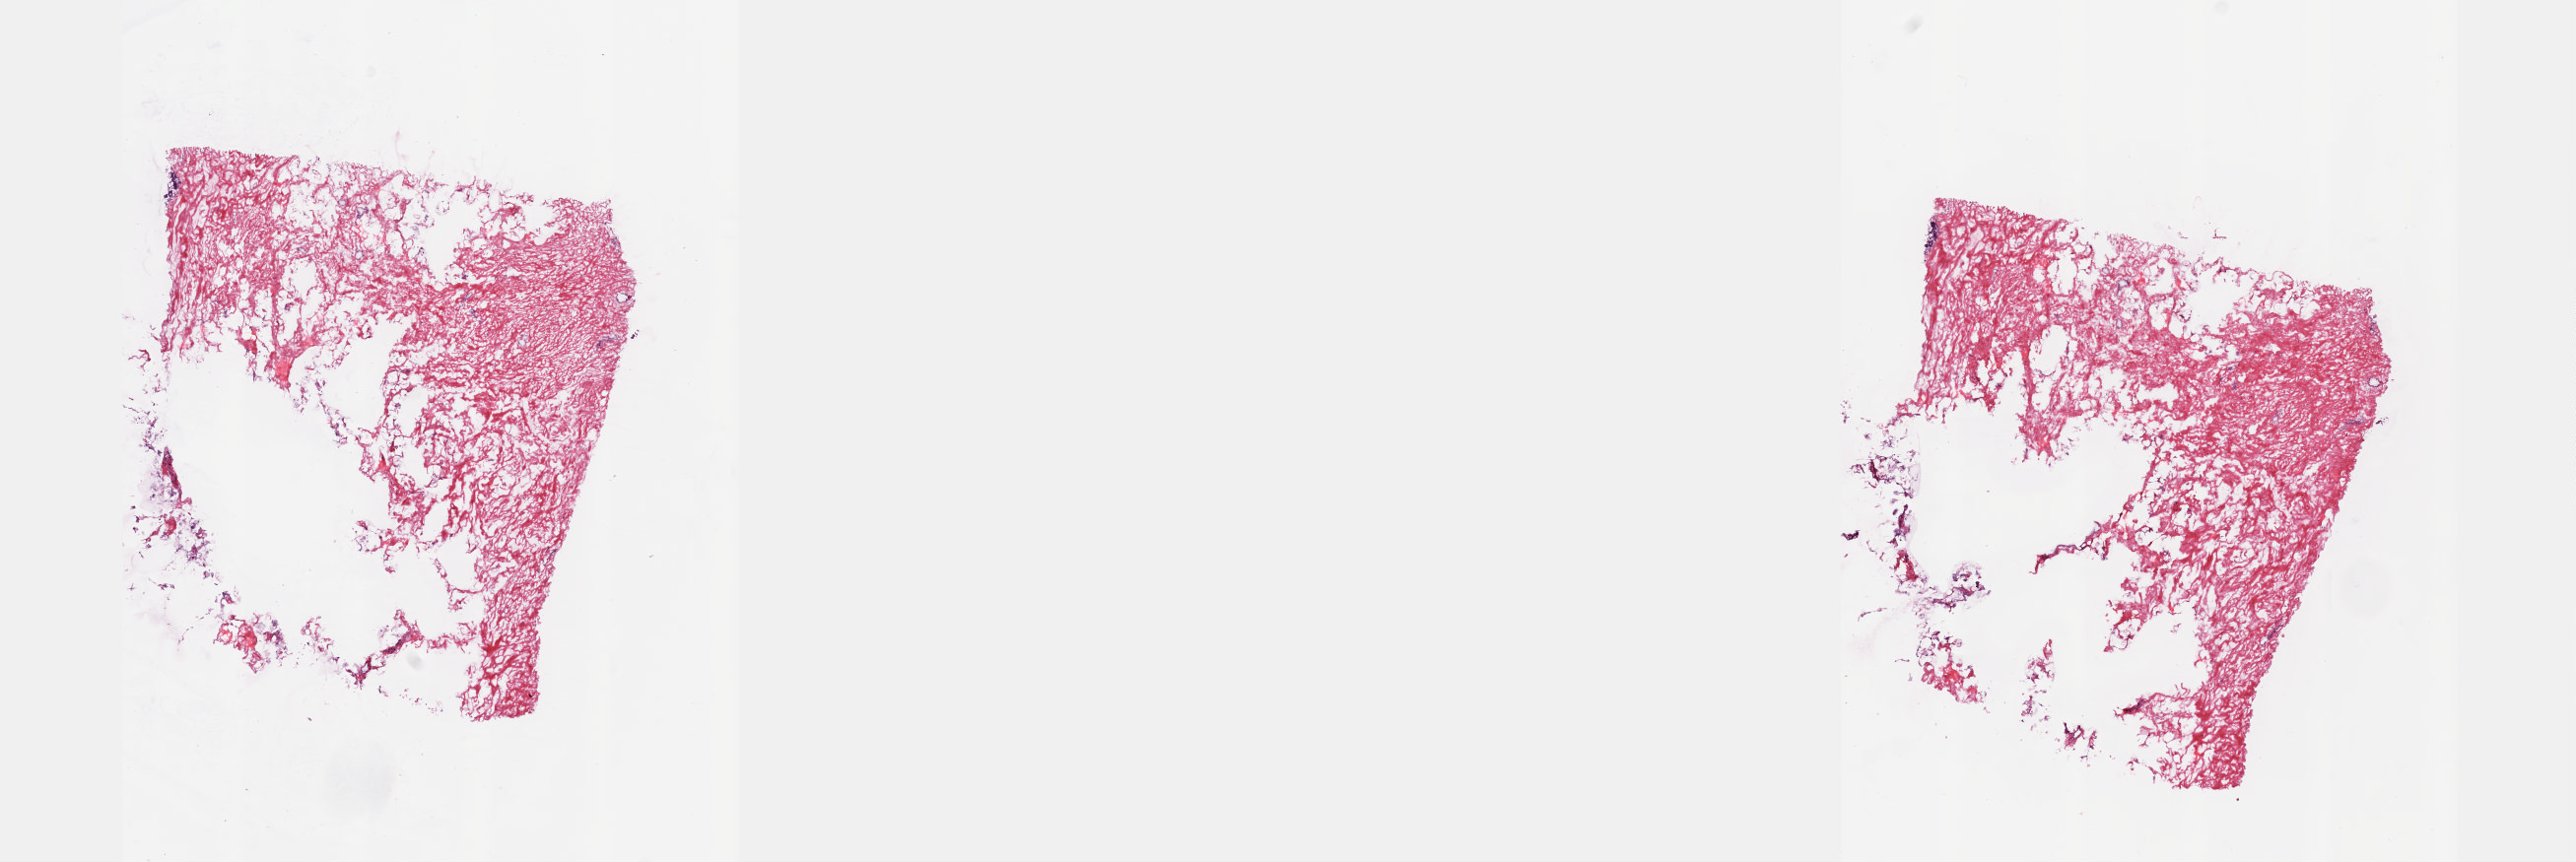
Whole-slide histology image, H&E, low-resolution overview of the scanned area, about 21.1 x 7.1 mm (from a 20x scan); frozen section; solid tissue normal (non-tumour tissue) sample from the breast. Patient: female, age at initial diagnosis 46 years. Pathologist review of this section (percent, as recorded): tumour cells 0%, tumour nuclei 0%, normal cells 100%, stromal cells 0%, necrosis 0%. Inflammatory infiltration, as recorded: lymphocyte infiltration 1%, monocyte infiltration 0%, neutrophil infiltration 0%.
* this section: solid tissue normal sample (biorepository sample class)
* patient diagnosis: Lobular carcinoma, NOS